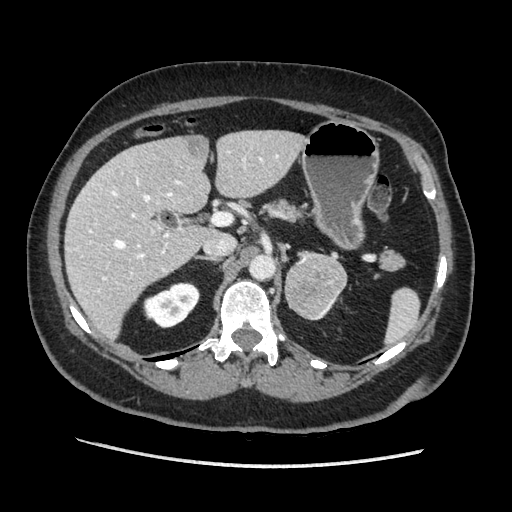
Contrast-enhanced abdominal CT, one axial slice. Position 122 of 203 along the scan axis. Soft-tissue window (W 400 / L 40 HU). 1.25 mm slice thickness. 512 × 512 image matrix, field of view 360 × 360 mm. Female patient. Case-level facts recorded for this patient, not image findings: diagnosis: adrenocortical carcinoma; tumour side: left adrenal; tumour size at pathology: 6.5 cm; Ki-67 index: 22 %; stage (as recorded): 2.
Outlined on this slice (semi-automatic segmentation, software-assisted and operator-edited):
- mass: bounding box [x1, y1, x2, y2] px = [285, 252, 348, 319]